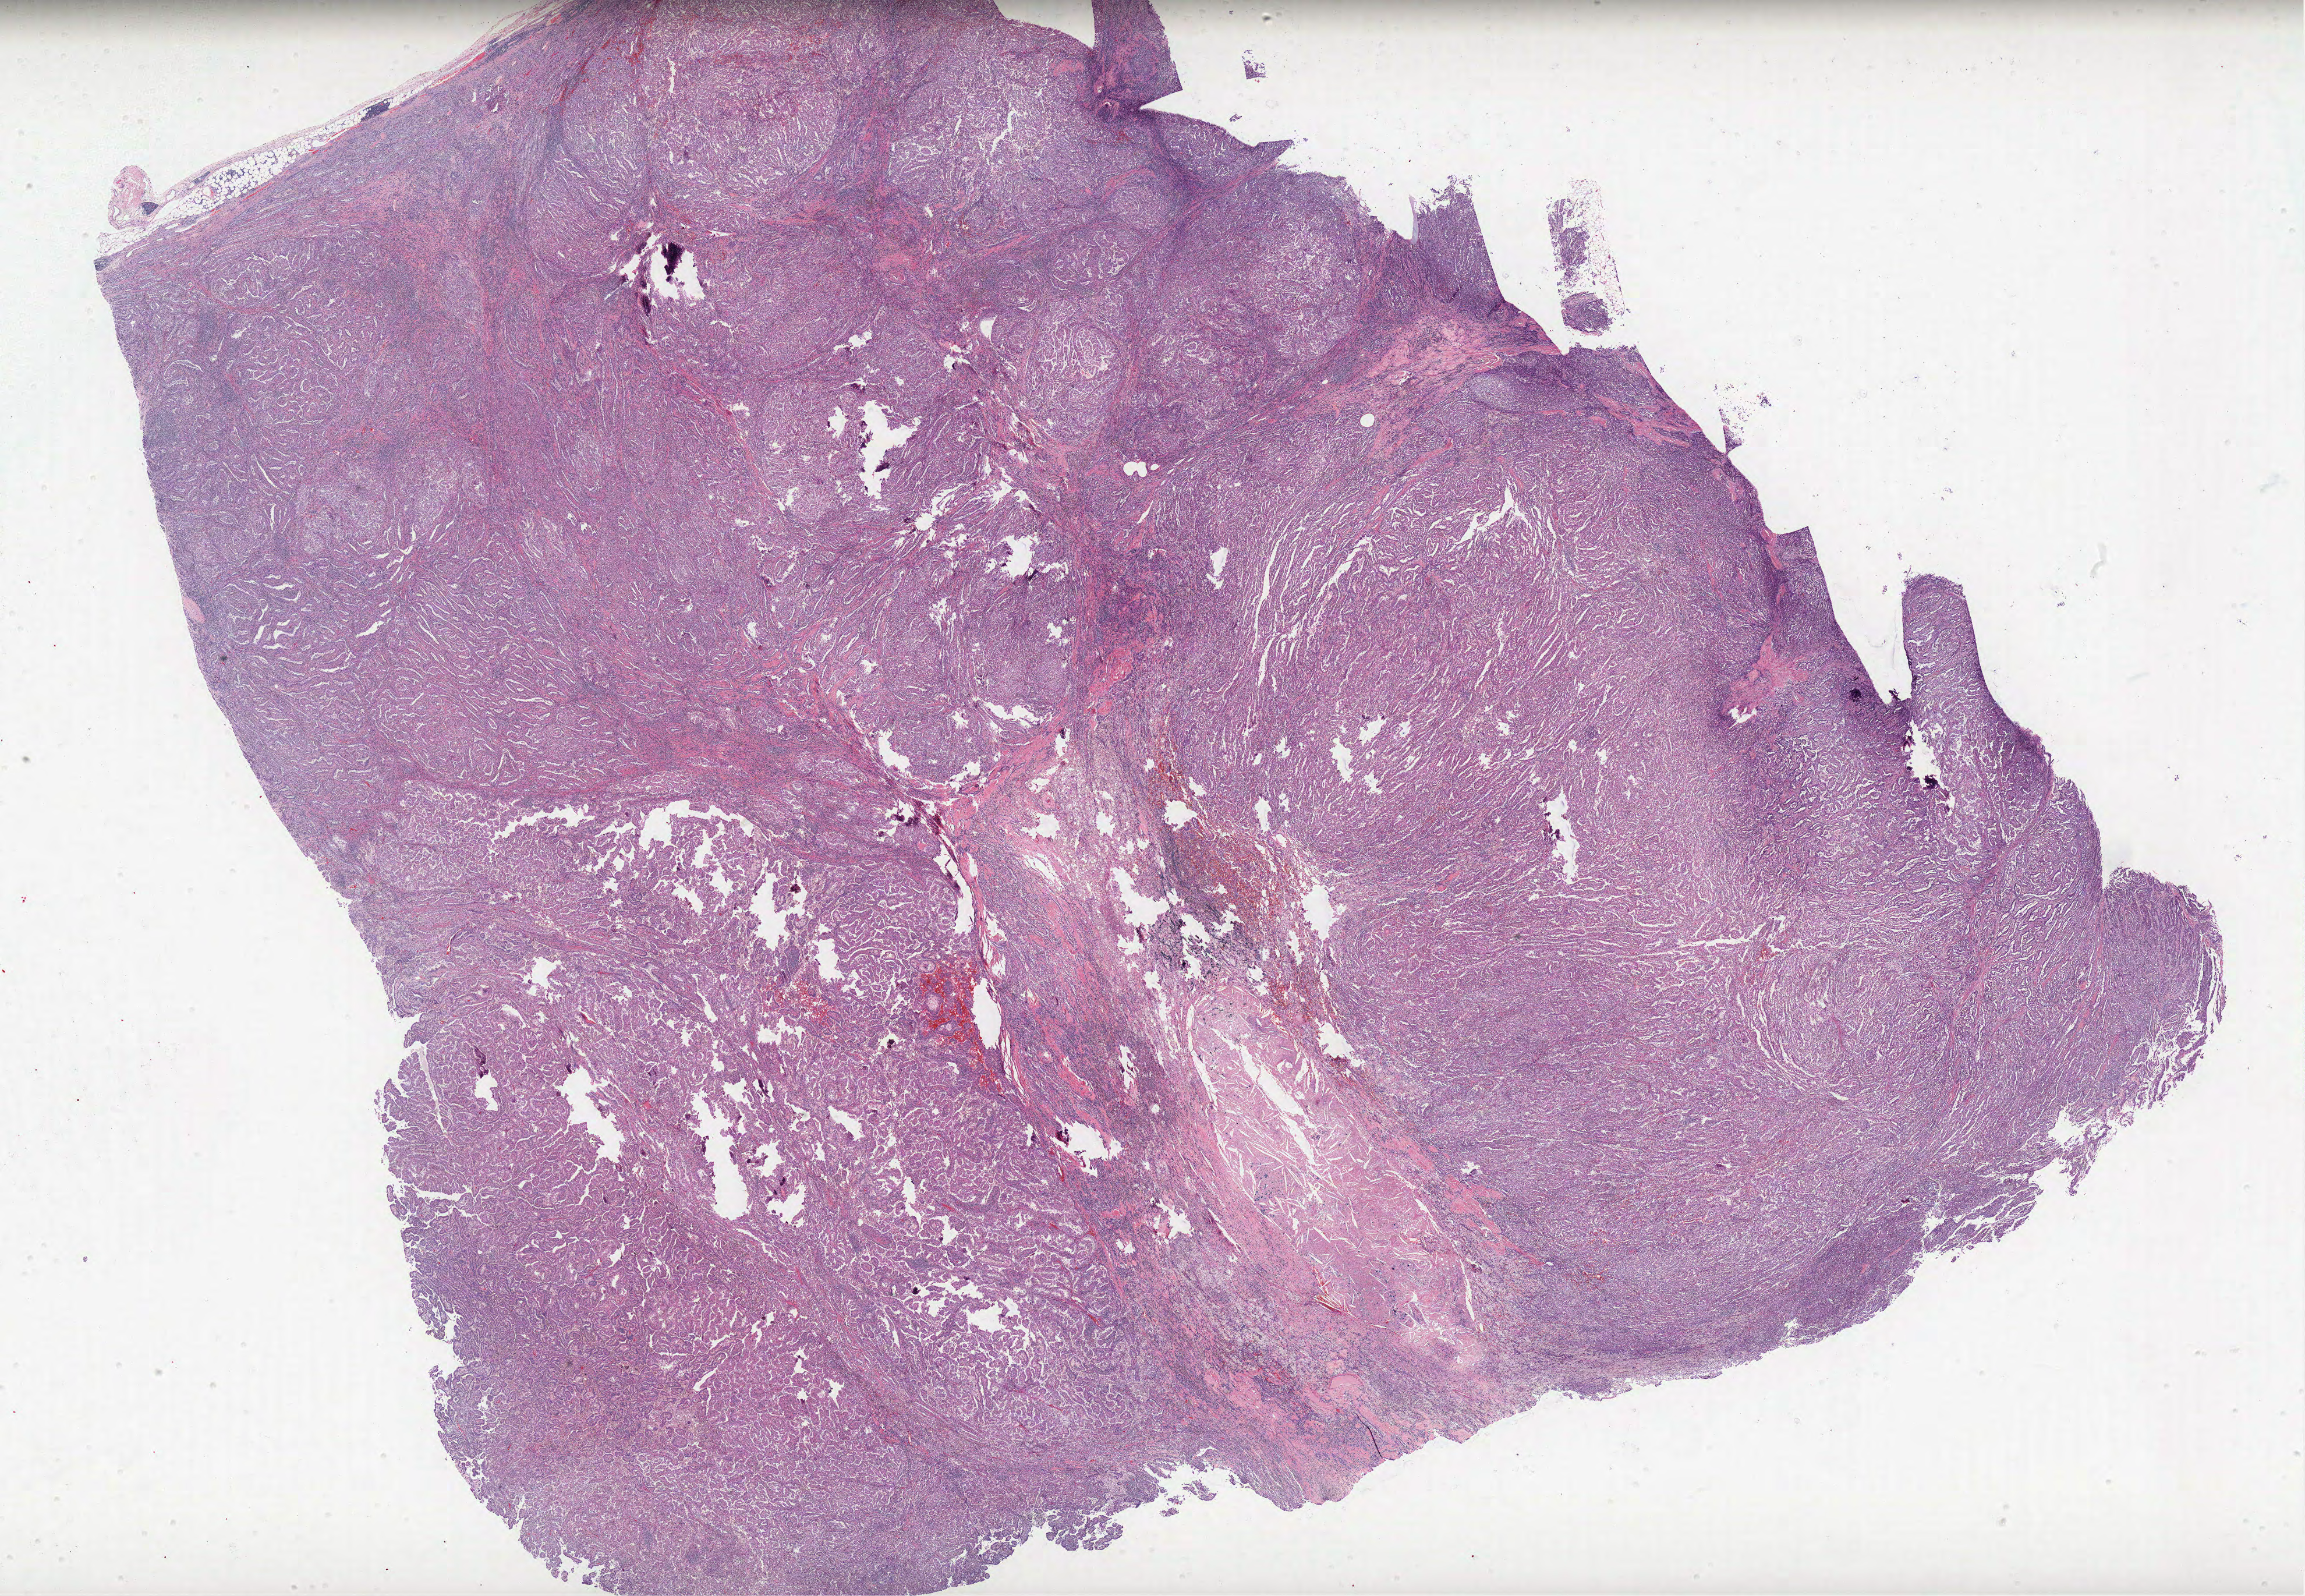
Hematoxylin and eosin (H&E) stained whole-slide image, whole scanned area (about 31.6 x 21.9 mm, from a 40x scan) shown as a low-resolution overview, formalin-fixed paraffin-embedded (FFPE) diagnostic section, kidney, primary tumour sample. Female, age 74 years at initial diagnosis.
AJCC pathologic stage: I. Lymph nodes positive (case pathology): 0 of 2 examined. TNM: T1a N0 M0. Pathologic diagnosis: Papillary adenocarcinoma, NOS. Laterality: right.